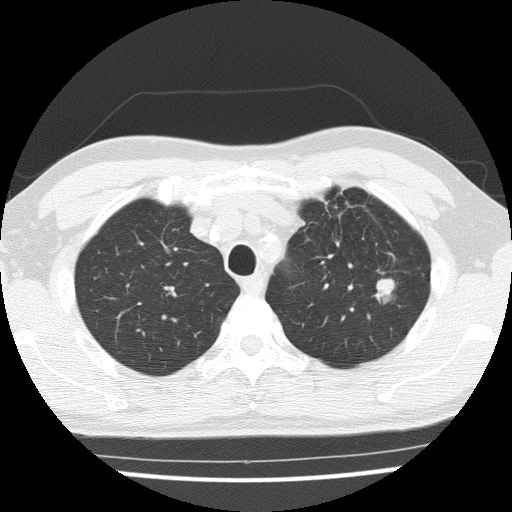
Low-dose screening chest CT, one axial slice; position 118 of 154 along the scan axis; reconstruction kernel FC51; lung window (W 1500 / L -600 HU); 2 mm slice thickness; 512 × 512 image matrix, field of view 330 × 330 mm.
Annotated regions visible in this slice (manually delineated by an expert):
- lesion 1 (tumor, upper lobe of left lung): box from (x=375, y=279) to (x=394, y=303) px